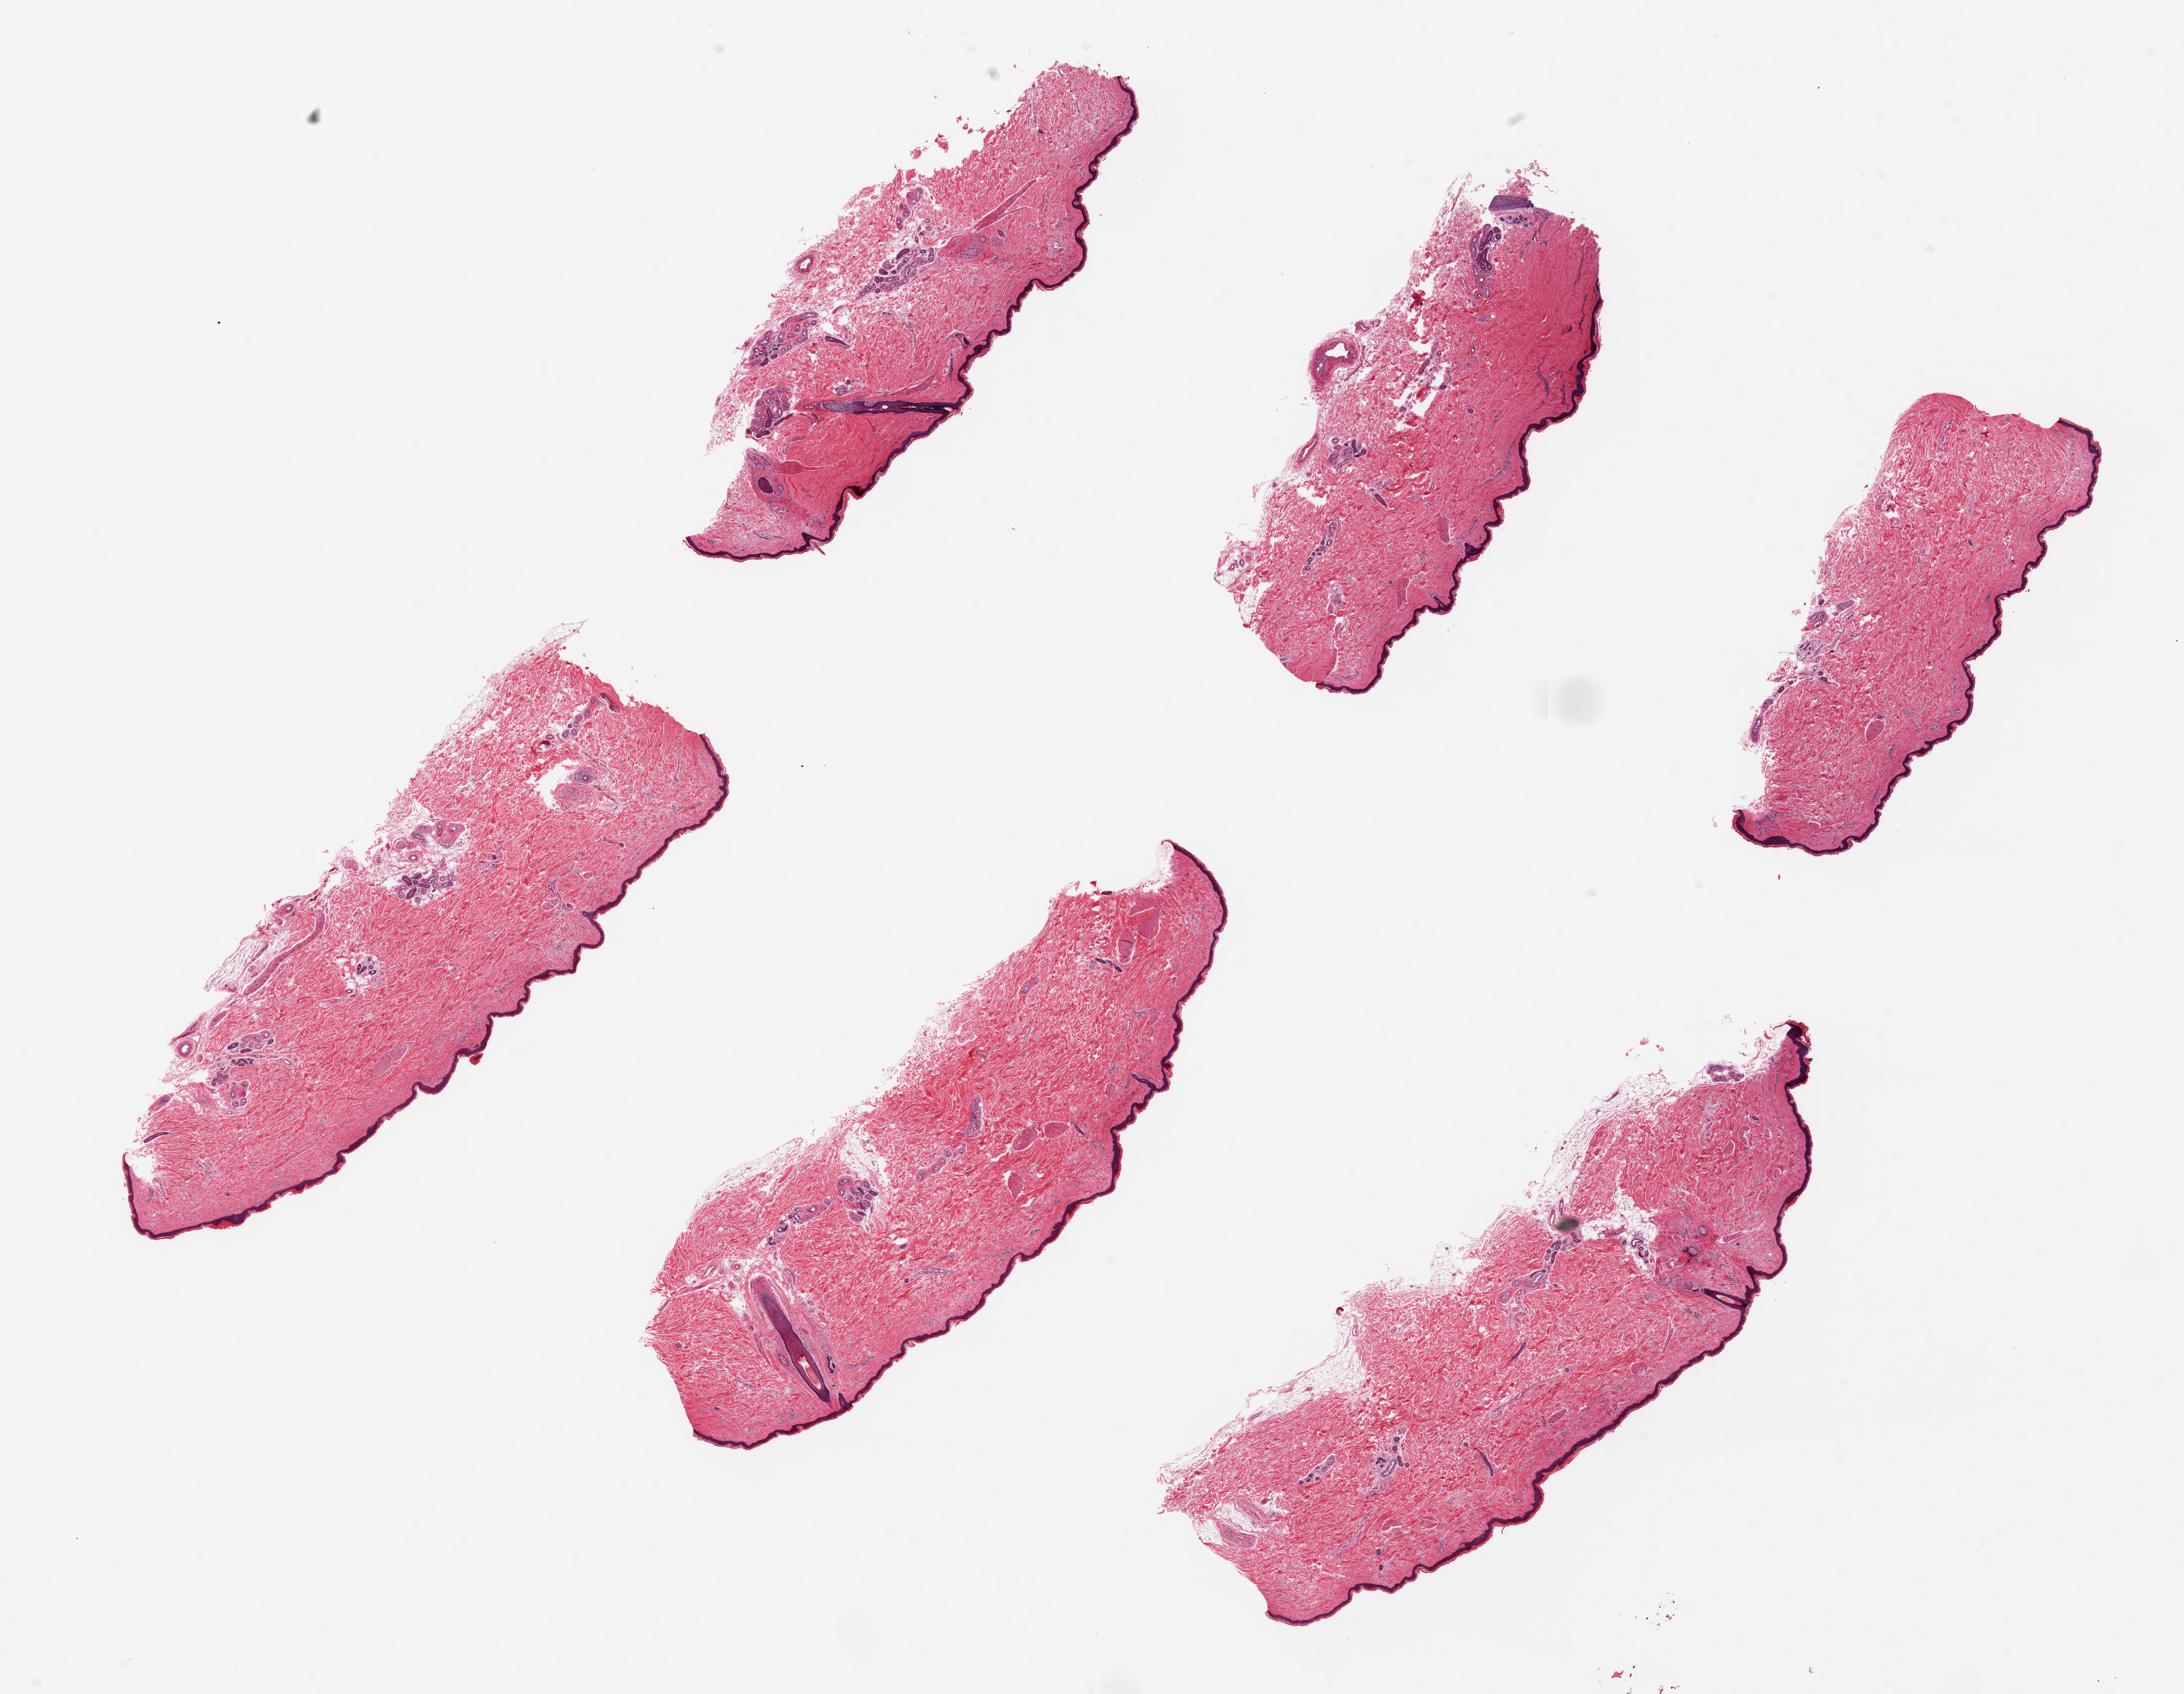
Digitized haematoxylin and eosin-stained section, a low-resolution overview of the entire scanned area, about 23.6 x 18.3 mm. PAXgene-fixed, paraffin-embedded tissue. Target tissue: skin of lower leg. Donor tissue sample. Donor sex: male.
Review note (as recorded): 6 pieces, up to 8.5x3mm; subcutaneous fat is well trimmed.